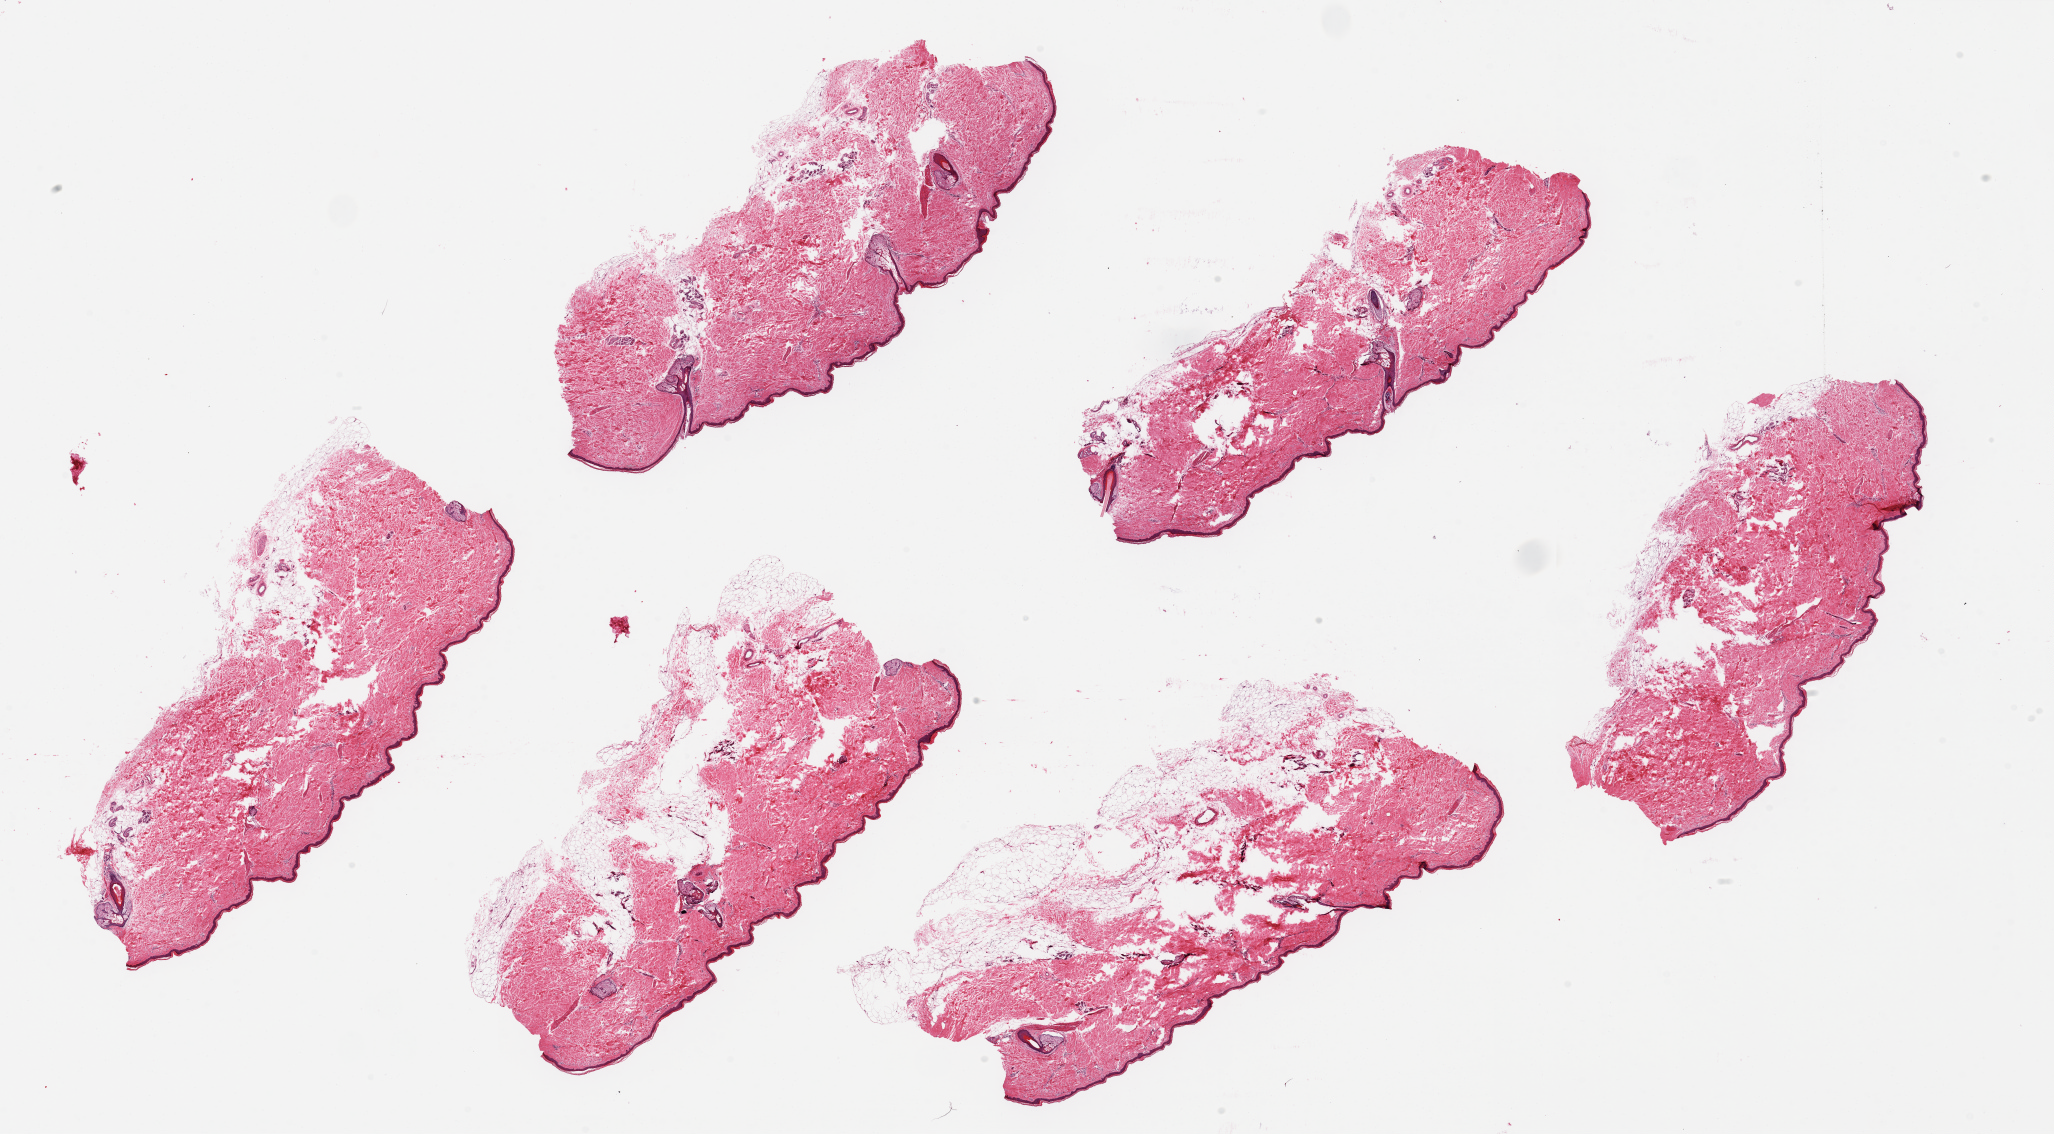
H&E whole-slide image, brightfield, low-resolution overview of the scanned area, about 32.5 x 17.9 mm. PAXgene-fixed, paraffin-embedded tissue. Sampled site (target tissue): skin of lower leg. Donor tissue sample. Donor: male.
- pathologist's review note for this sample: 6 pieces, up to 9x3.7 mm